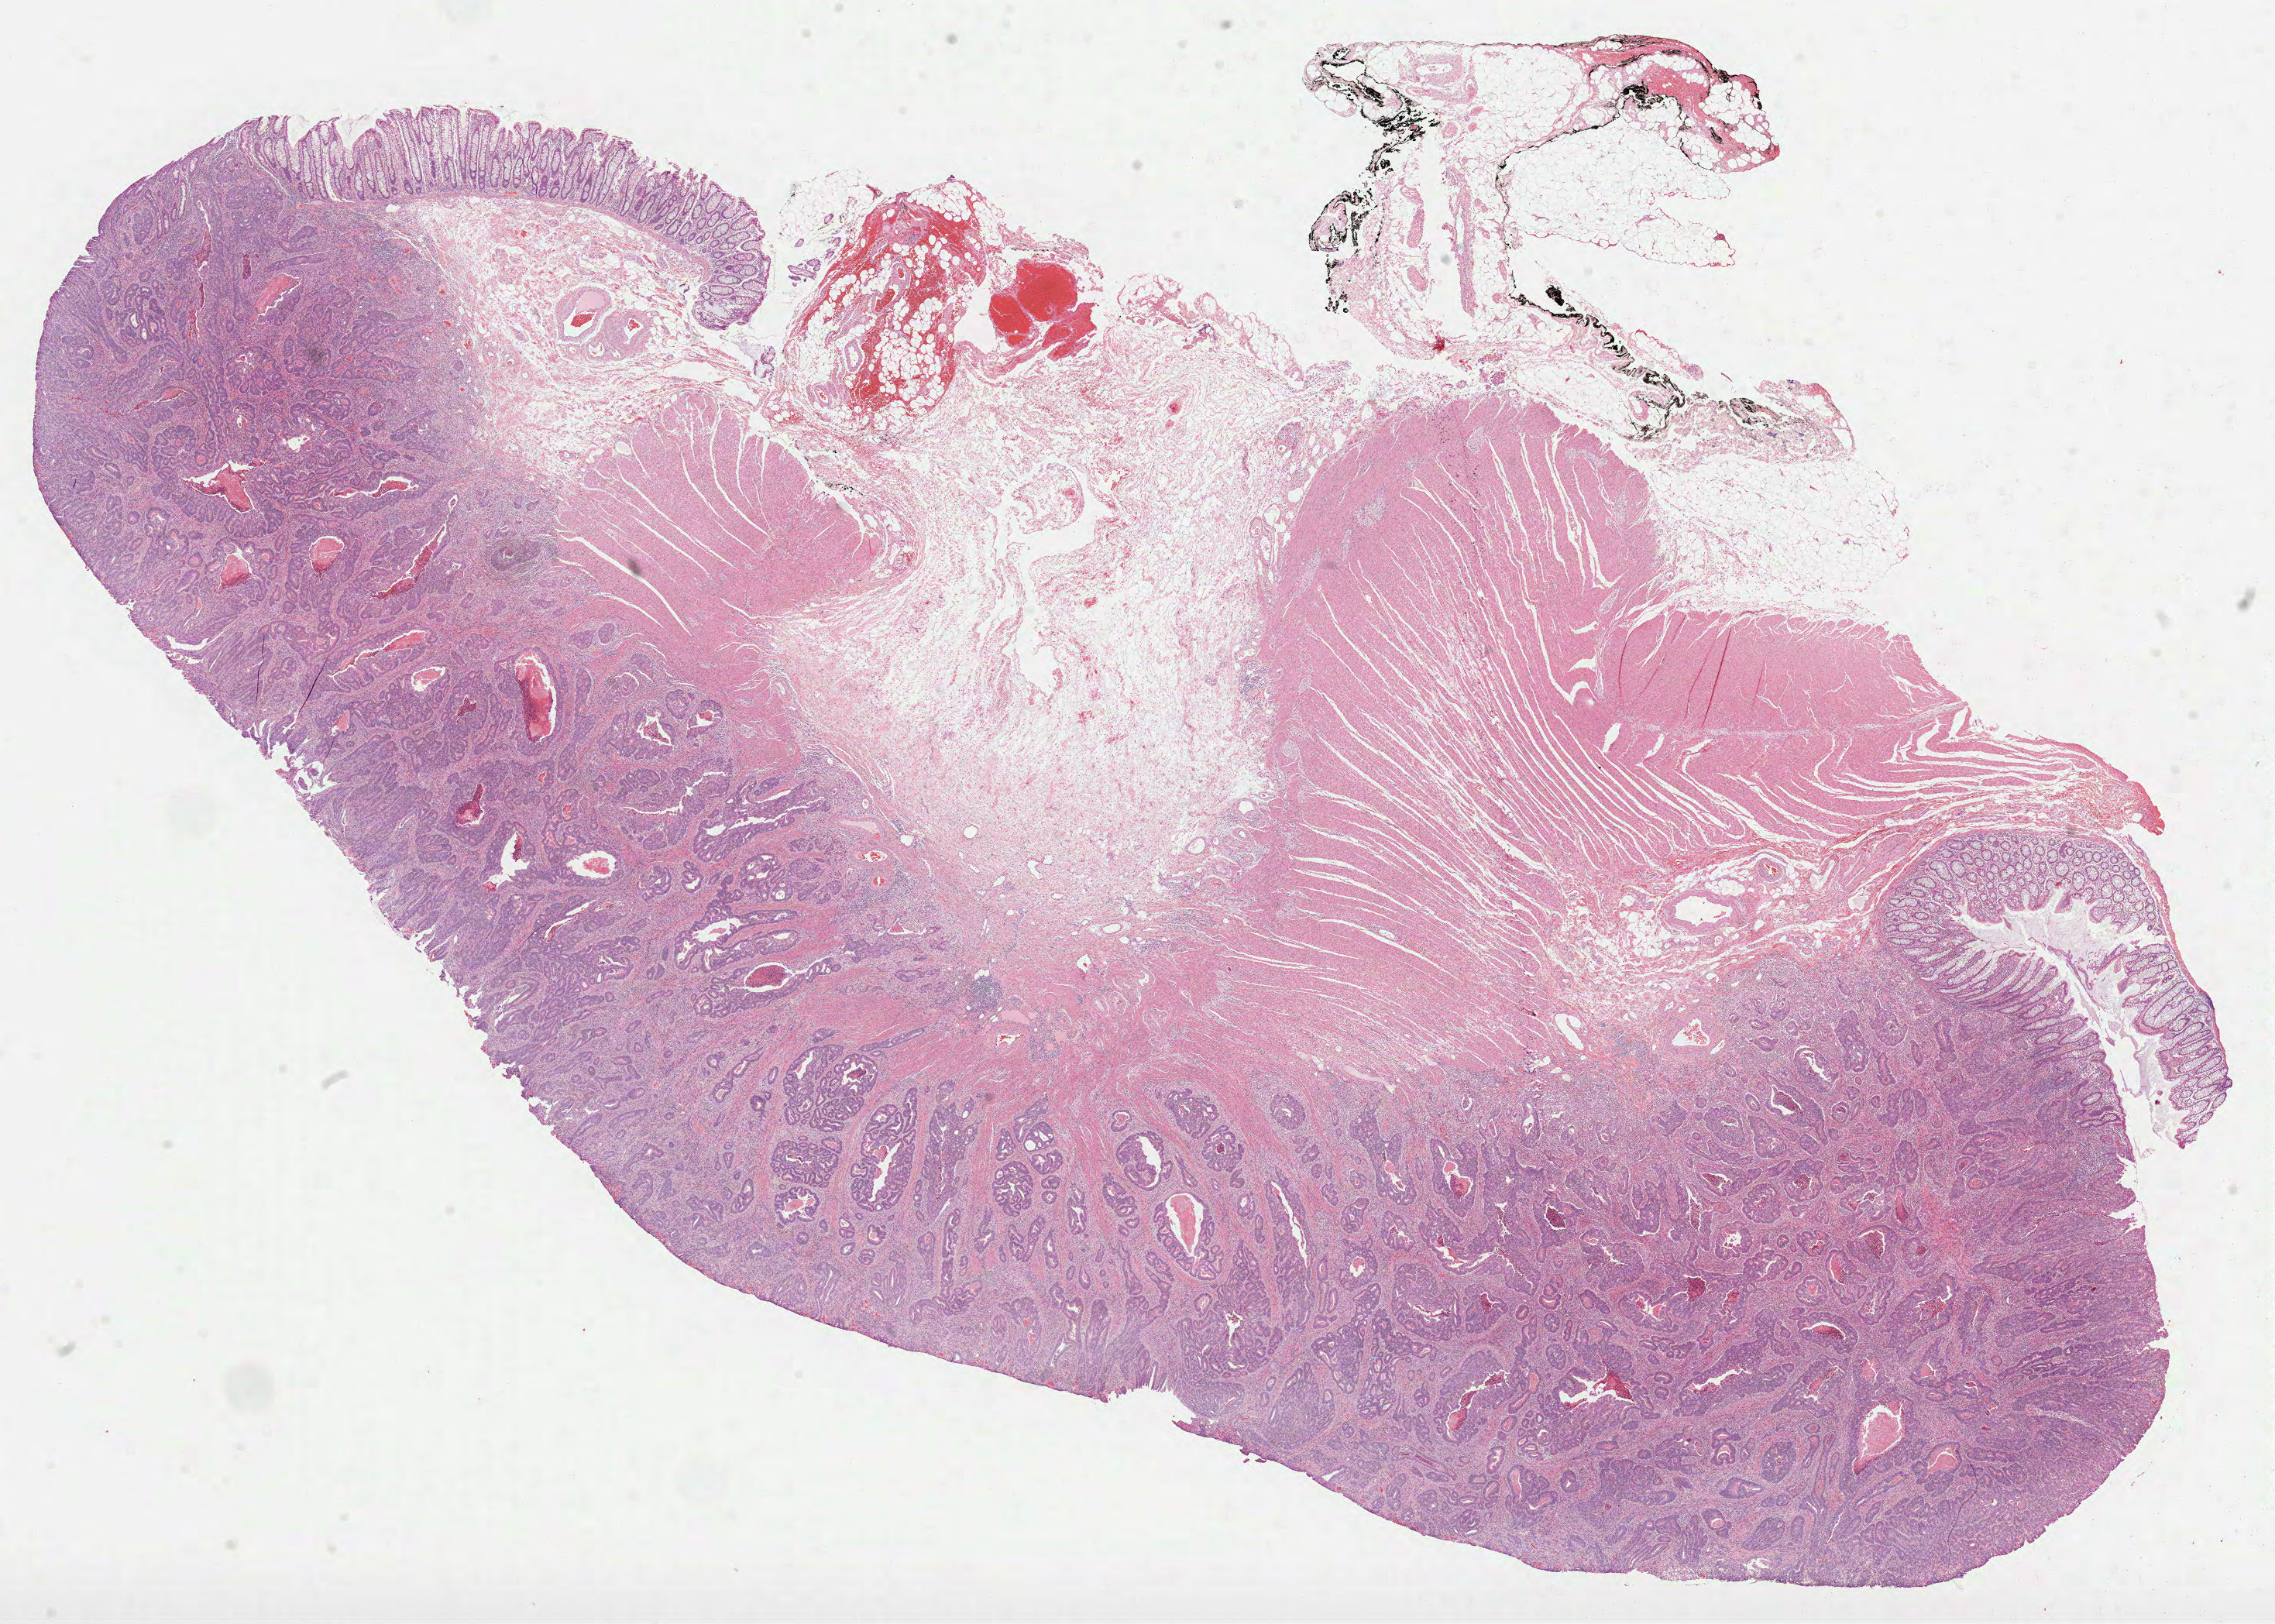
Digitized Hematoxylin and eosin (H&E) stained tissue section (whole slide) — shown as a low-resolution overview of the whole scanned area (about 23.7 x 16.9 mm, acquisition: 40x scan). FFPE section. Colon, primary tumour sample. Male, age 71 years at initial diagnosis.
Diagnosis: Adenocarcinoma, NOS (ascending colon).